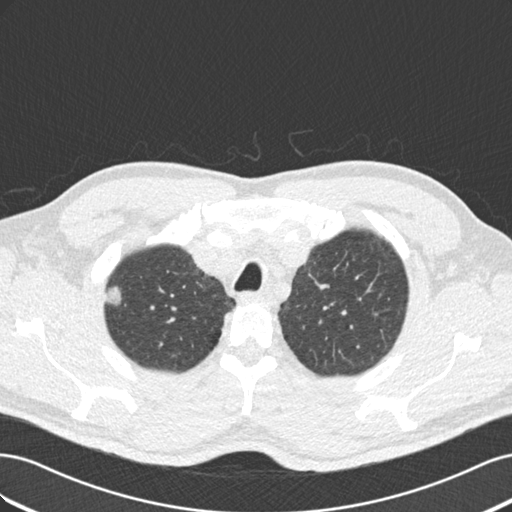
Axial slice from a low-dose chest CT screening exam. Second annual screen. Lung window (W 1500 / L -600 HU). Standard (soft-tissue) reconstruction kernel (B30f). Male participant, aged 56 years at enrolment. Current smoker at enrolment.
Lesion marked by an expert reader, bounding box [x1, y1, x2, y2] px = [93, 279, 133, 313]. Screening reader's record for this exam (one nodule recorded; not confirmed to be the boxed lesion): non-calcified nodule or mass ≥4 mm, right upper lobe, 13 × 12 mm, smooth margins, mixed attenuation, pre-existing on the prior screen: yes; interval growth: yes. Participant outcome: lung cancer diagnosed 174 days after this screen — bronchiolo-alveolar carcinoma, non-mucinous, right upper lobe, moderately differentiated (G2), stage IIIB (AJCC 6th edition), 10 mm at pathology.